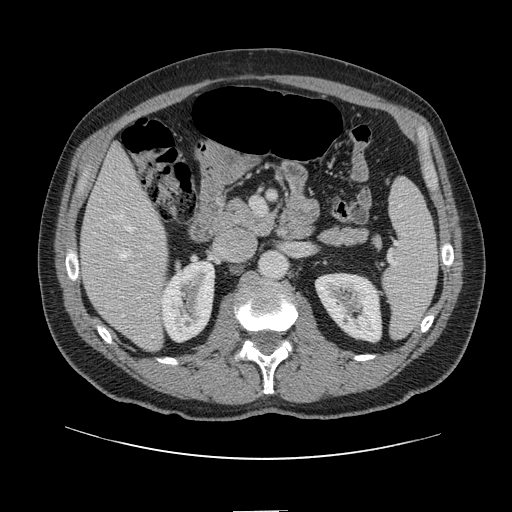
Contrast-enhanced abdominal CT, one axial slice. Position 50 of 161 along the scan axis. 120 kVp. Intravenous contrast given. Soft-tissue window (W 400 / L 40 HU). 2.5 mm slice thickness. 512 × 512 image matrix. Male patient, age 66 years. Case-level facts recorded for this patient, not image findings: diagnosis: colorectal cancer liver metastases, imaged before liver resection; multiple liver metastases: no; largest metastasis: 3.5 cm; disease in both lobes: no.
Structures marked on this image (outlined manually by an expert reader):
- hepatic veins: bounding box [x1, y1, x2, y2] px = [115, 213, 133, 259]
- liver: [81, 148, 167, 349]
- planned liver remnant (the part of the liver to remain after resection): [81, 149, 161, 276]
- portal vein (with intrahepatic branches): [129, 244, 153, 299]